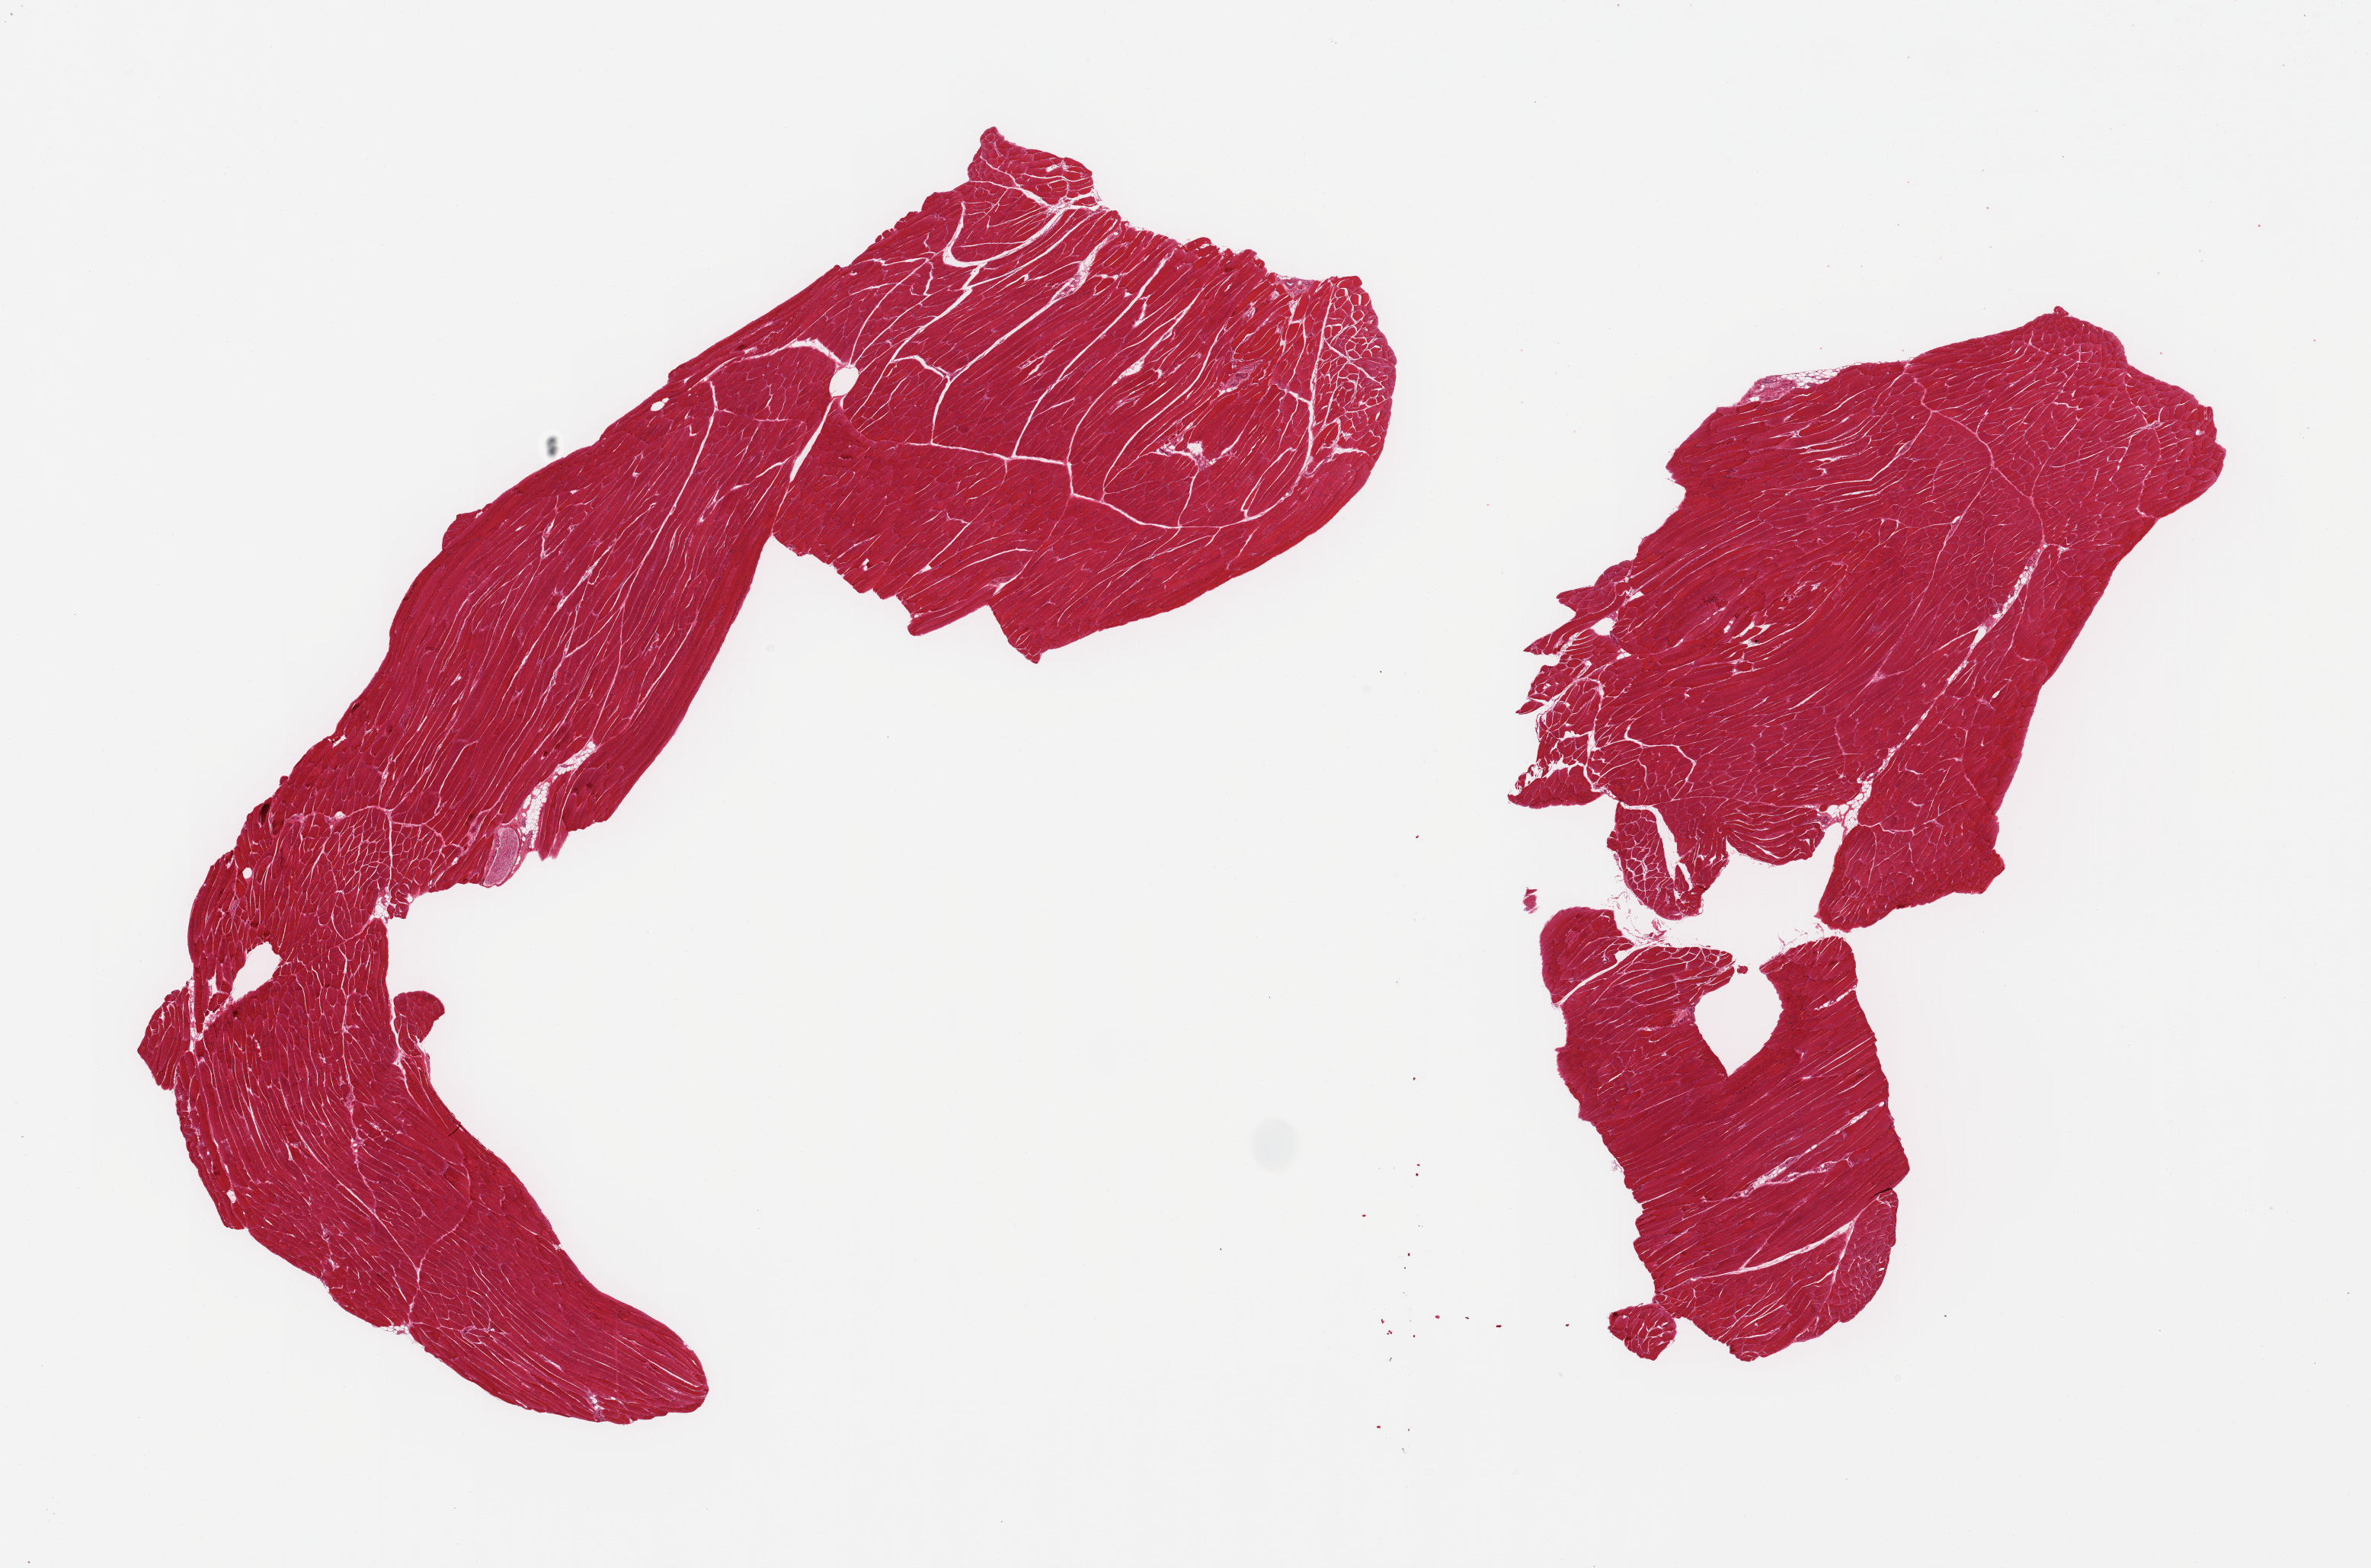
Digitized H&E-stained section — whole scanned area (about 24.6 x 16.3 mm) shown as a low-resolution overview. PAXgene-fixed paraffin-embedded (PFPE) section. Sampled site (target tissue): skeletal muscle. Tissue donor sample. Donor: male.
Pathologist's review note for this sample: 2 pieces; well trimmed.